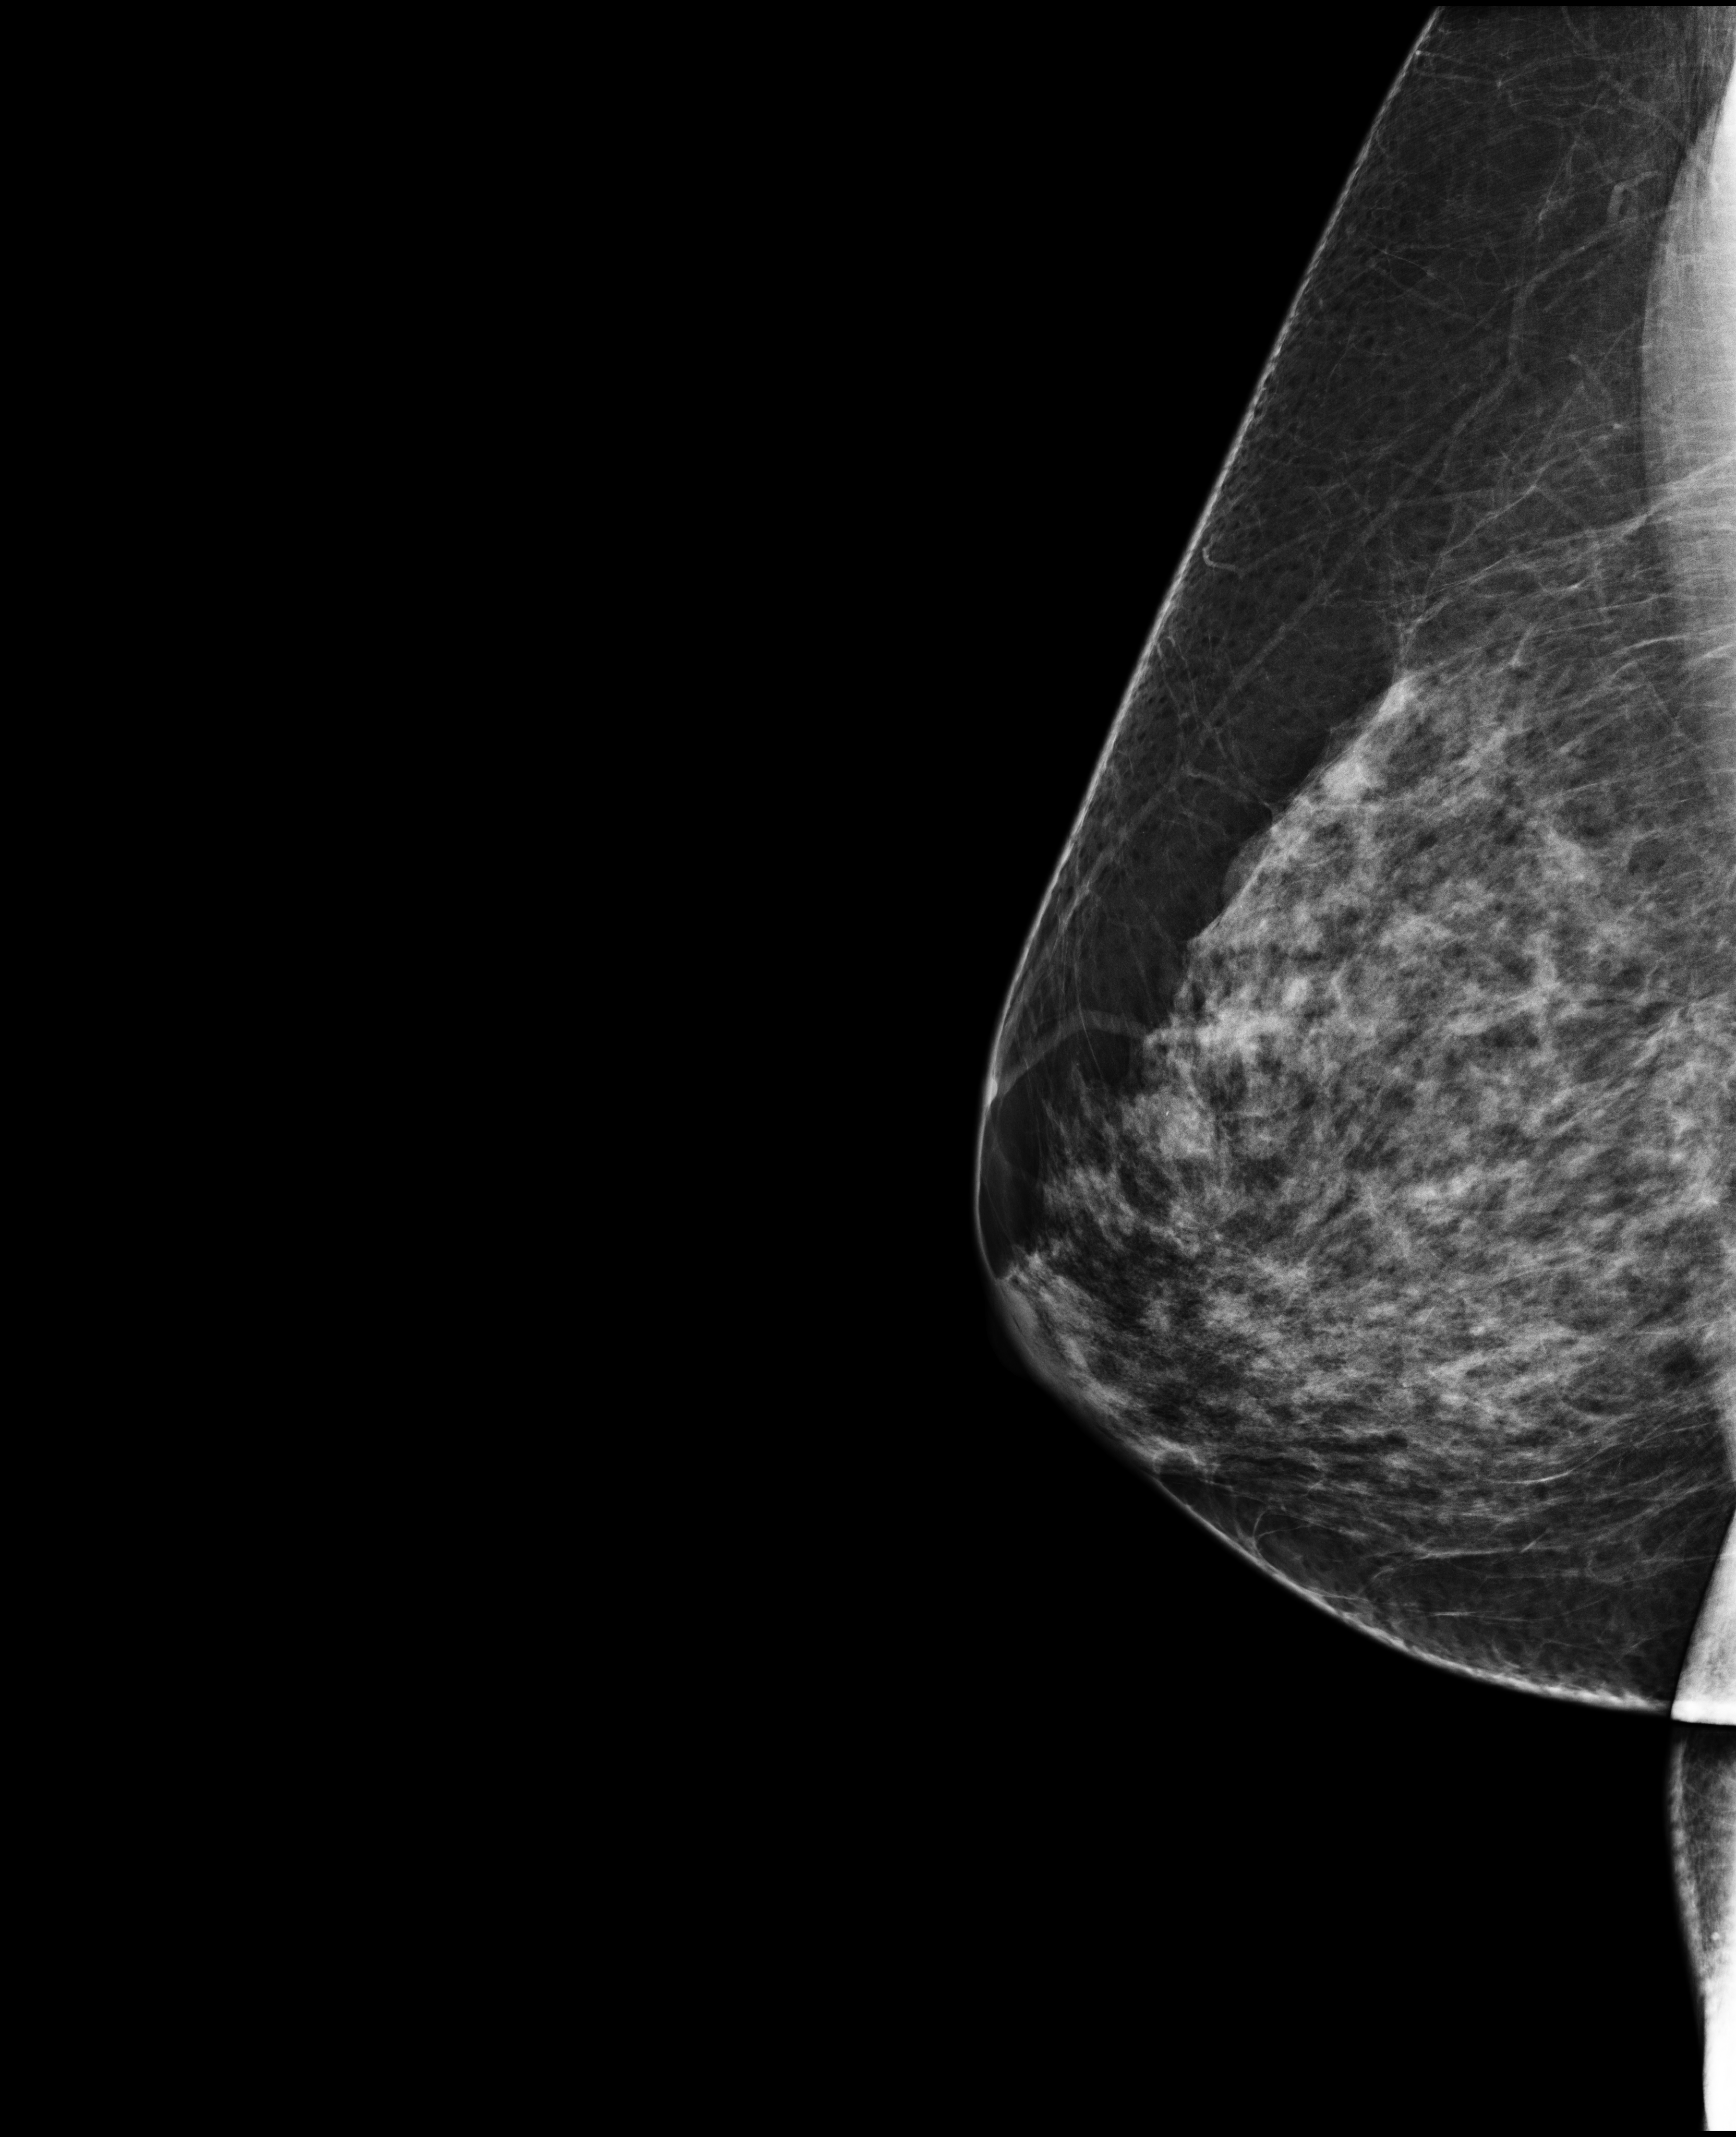
Screening examination. Patient: female, 53 years.
Image type: full-field digital mammogram. Breast: right. Projection: mediolateral oblique (MLO) view.